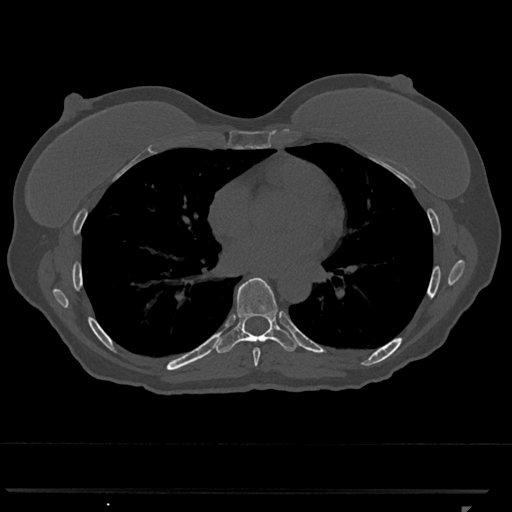
CT including the spine, one axial slice. Slice 677 of 793 in the series (ordered by position). Reconstruction kernel Br40s/3. Bone window (W 1800 / L 400 HU). 512 × 512 image matrix, field of view 380 × 380 mm. Patient: female, 62 years. Case-level facts recorded for this patient, not image findings: primary cancer: renal.
Annotated regions visible in this slice (semi-automatic segmentation, software-assisted and operator-edited):
- T7 vertebra: bounding box [x1, y1, x2, y2] px = [253, 348, 261, 366]
- T8 vertebra: [214, 277, 298, 353]